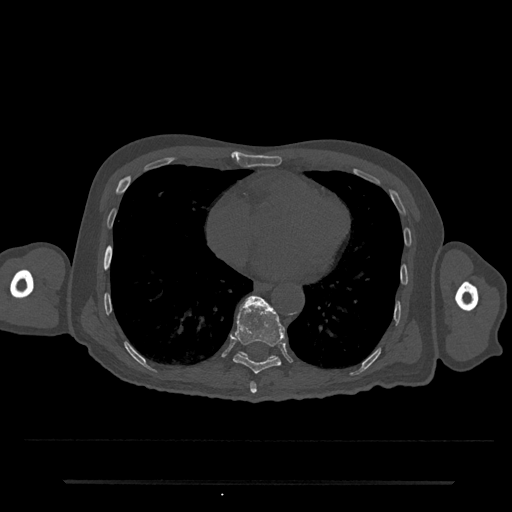
CT including the spine, one axial slice. Slice 358 of 797 in the series (ordered by position). 120 kVp. Bone window (W 1800 / L 400 HU). 0.5 mm slice thickness. 512 × 512 image matrix, field of view 427 × 427 mm. Male patient, age 74 years. From the clinical record (not read from this slice): primary cancer: prostate.
Structures marked on this image (semi-automatic segmentation, software-assisted and operator-edited):
- T10 vertebra: bounding box (x1, y1, x2, y2) in pixels: (239, 352, 274, 358)
- T8 vertebra: (250, 382, 257, 394)
- T9 vertebra: (233, 296, 285, 374)